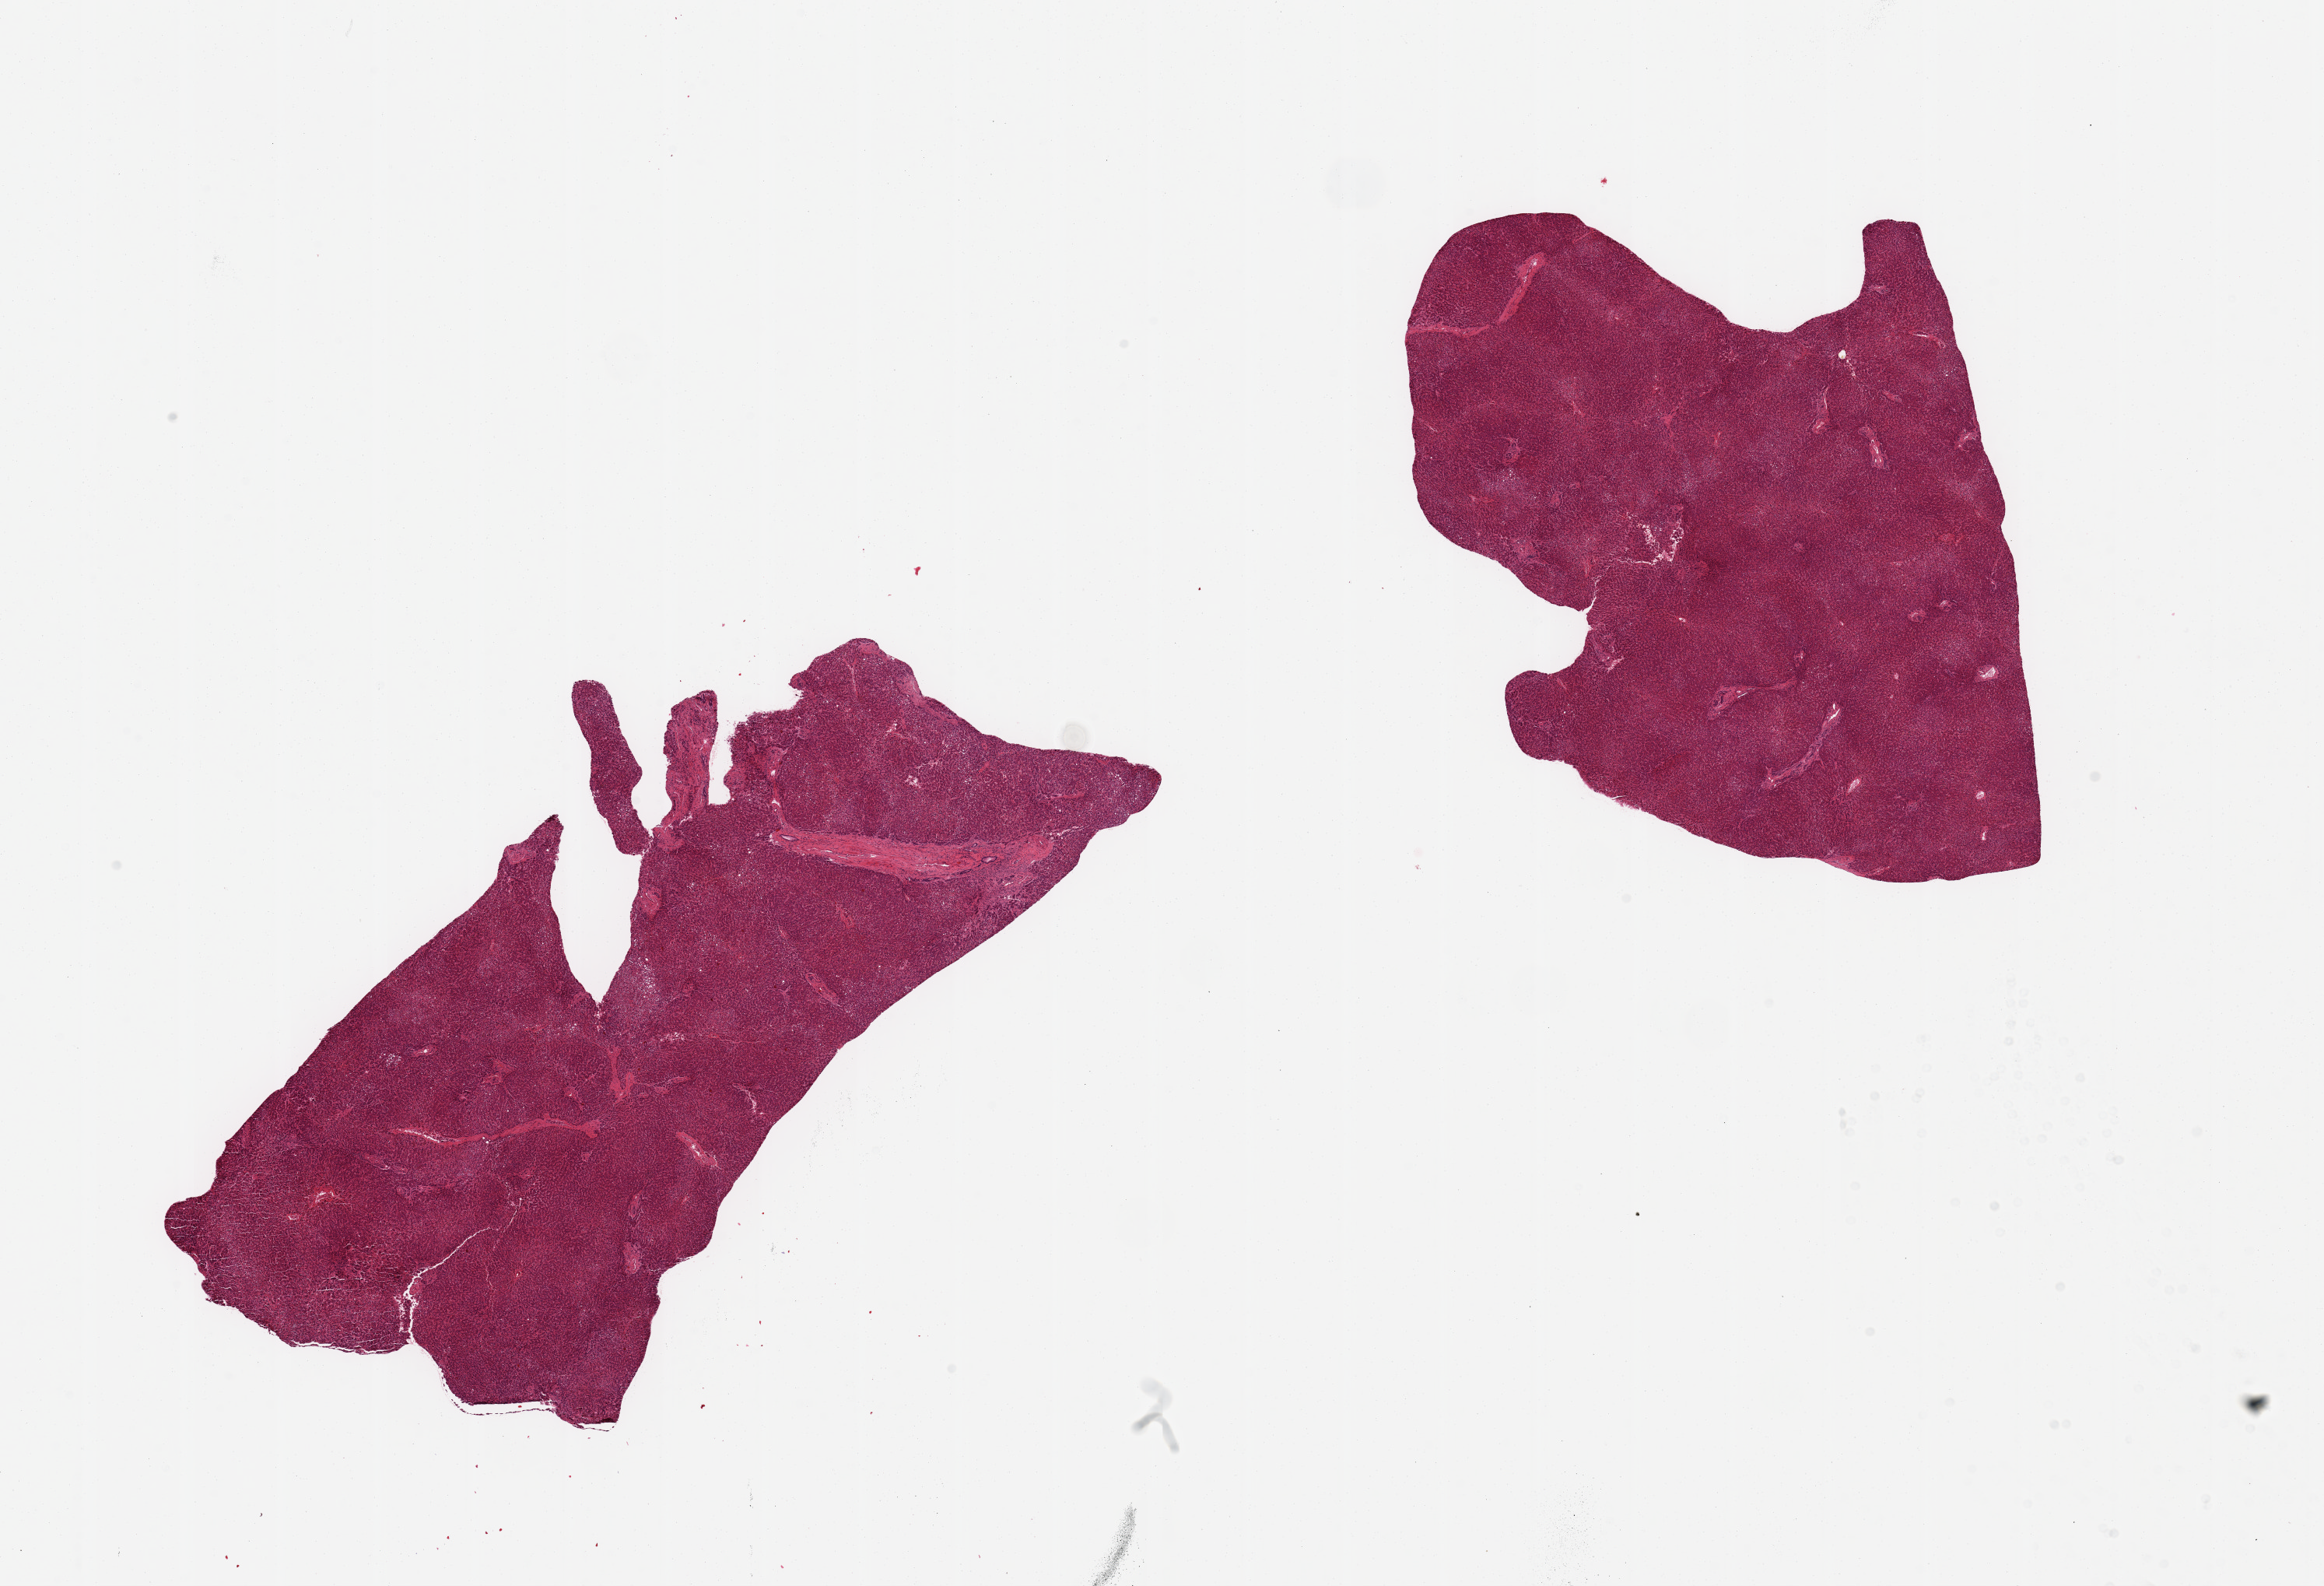
Digitized H&E-stained section — low-resolution overview of the scanned area, about 23.6 x 16.1 mm. PAXgene-fixed paraffin-embedded (PFPE) section. Sampled site (target tissue): liver. Donor tissue sample.
Review note (as recorded): 2 pieces, diffuse microvesicular steatosis, mild-moderate fibrosis.